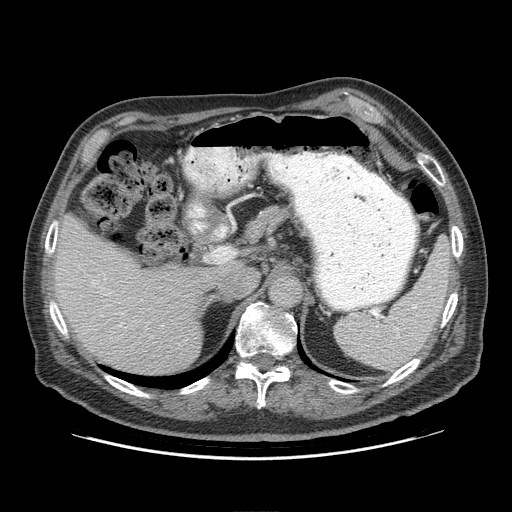
Contrast-enhanced abdominal CT (liver protocol), one axial slice; reconstruction kernel STANDARD; 140 kVp; soft-tissue window (W 400 / L 40 HU); 2.5 mm slice thickness; 512 × 512 image matrix. From the clinical record (not read from this slice): diagnosis: hepatocellular carcinoma (patient treated with transarterial chemoembolisation; whether this scan precedes or follows treatment is not stated here); TNM stage (as recorded): Stage-IVB; Child-Pugh class: A.
Annotated regions visible in this slice (semi-automatically segmented with operator editing):
- liver parenchyma outside the tumour (the mass and vessels are separate outlines, so this box may not span the whole liver): bounding box <54,214,212,374> (left, top, right, bottom; pixels)